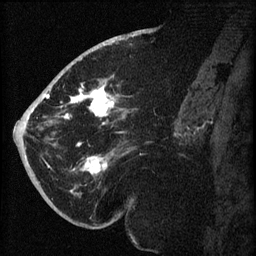
Breast MRI (dynamic contrast-enhanced), one sagittal slice. Position 35 of 60 along the scan axis. Dynamic contrast-enhanced series, image 2 of 3 at this slice position (ordered by acquisition). 1.5 T. TE 4.2 ms, TR 8.2 ms. 256 × 256 image matrix, field of view 180 × 180 mm. Female patient, age 71 years.
Structures marked on this image (semi-automatically segmented with operator editing):
- analysis volume of interest (the breast-tissue region the enhancement analysis was run in; not a lesion): bounding box [x1, y1, x2, y2] px = [40, 72, 137, 196]
- tumour enhancement mask (voxels above the 70 % enhancement threshold inside the analysis volume of interest): [43, 82, 124, 193]